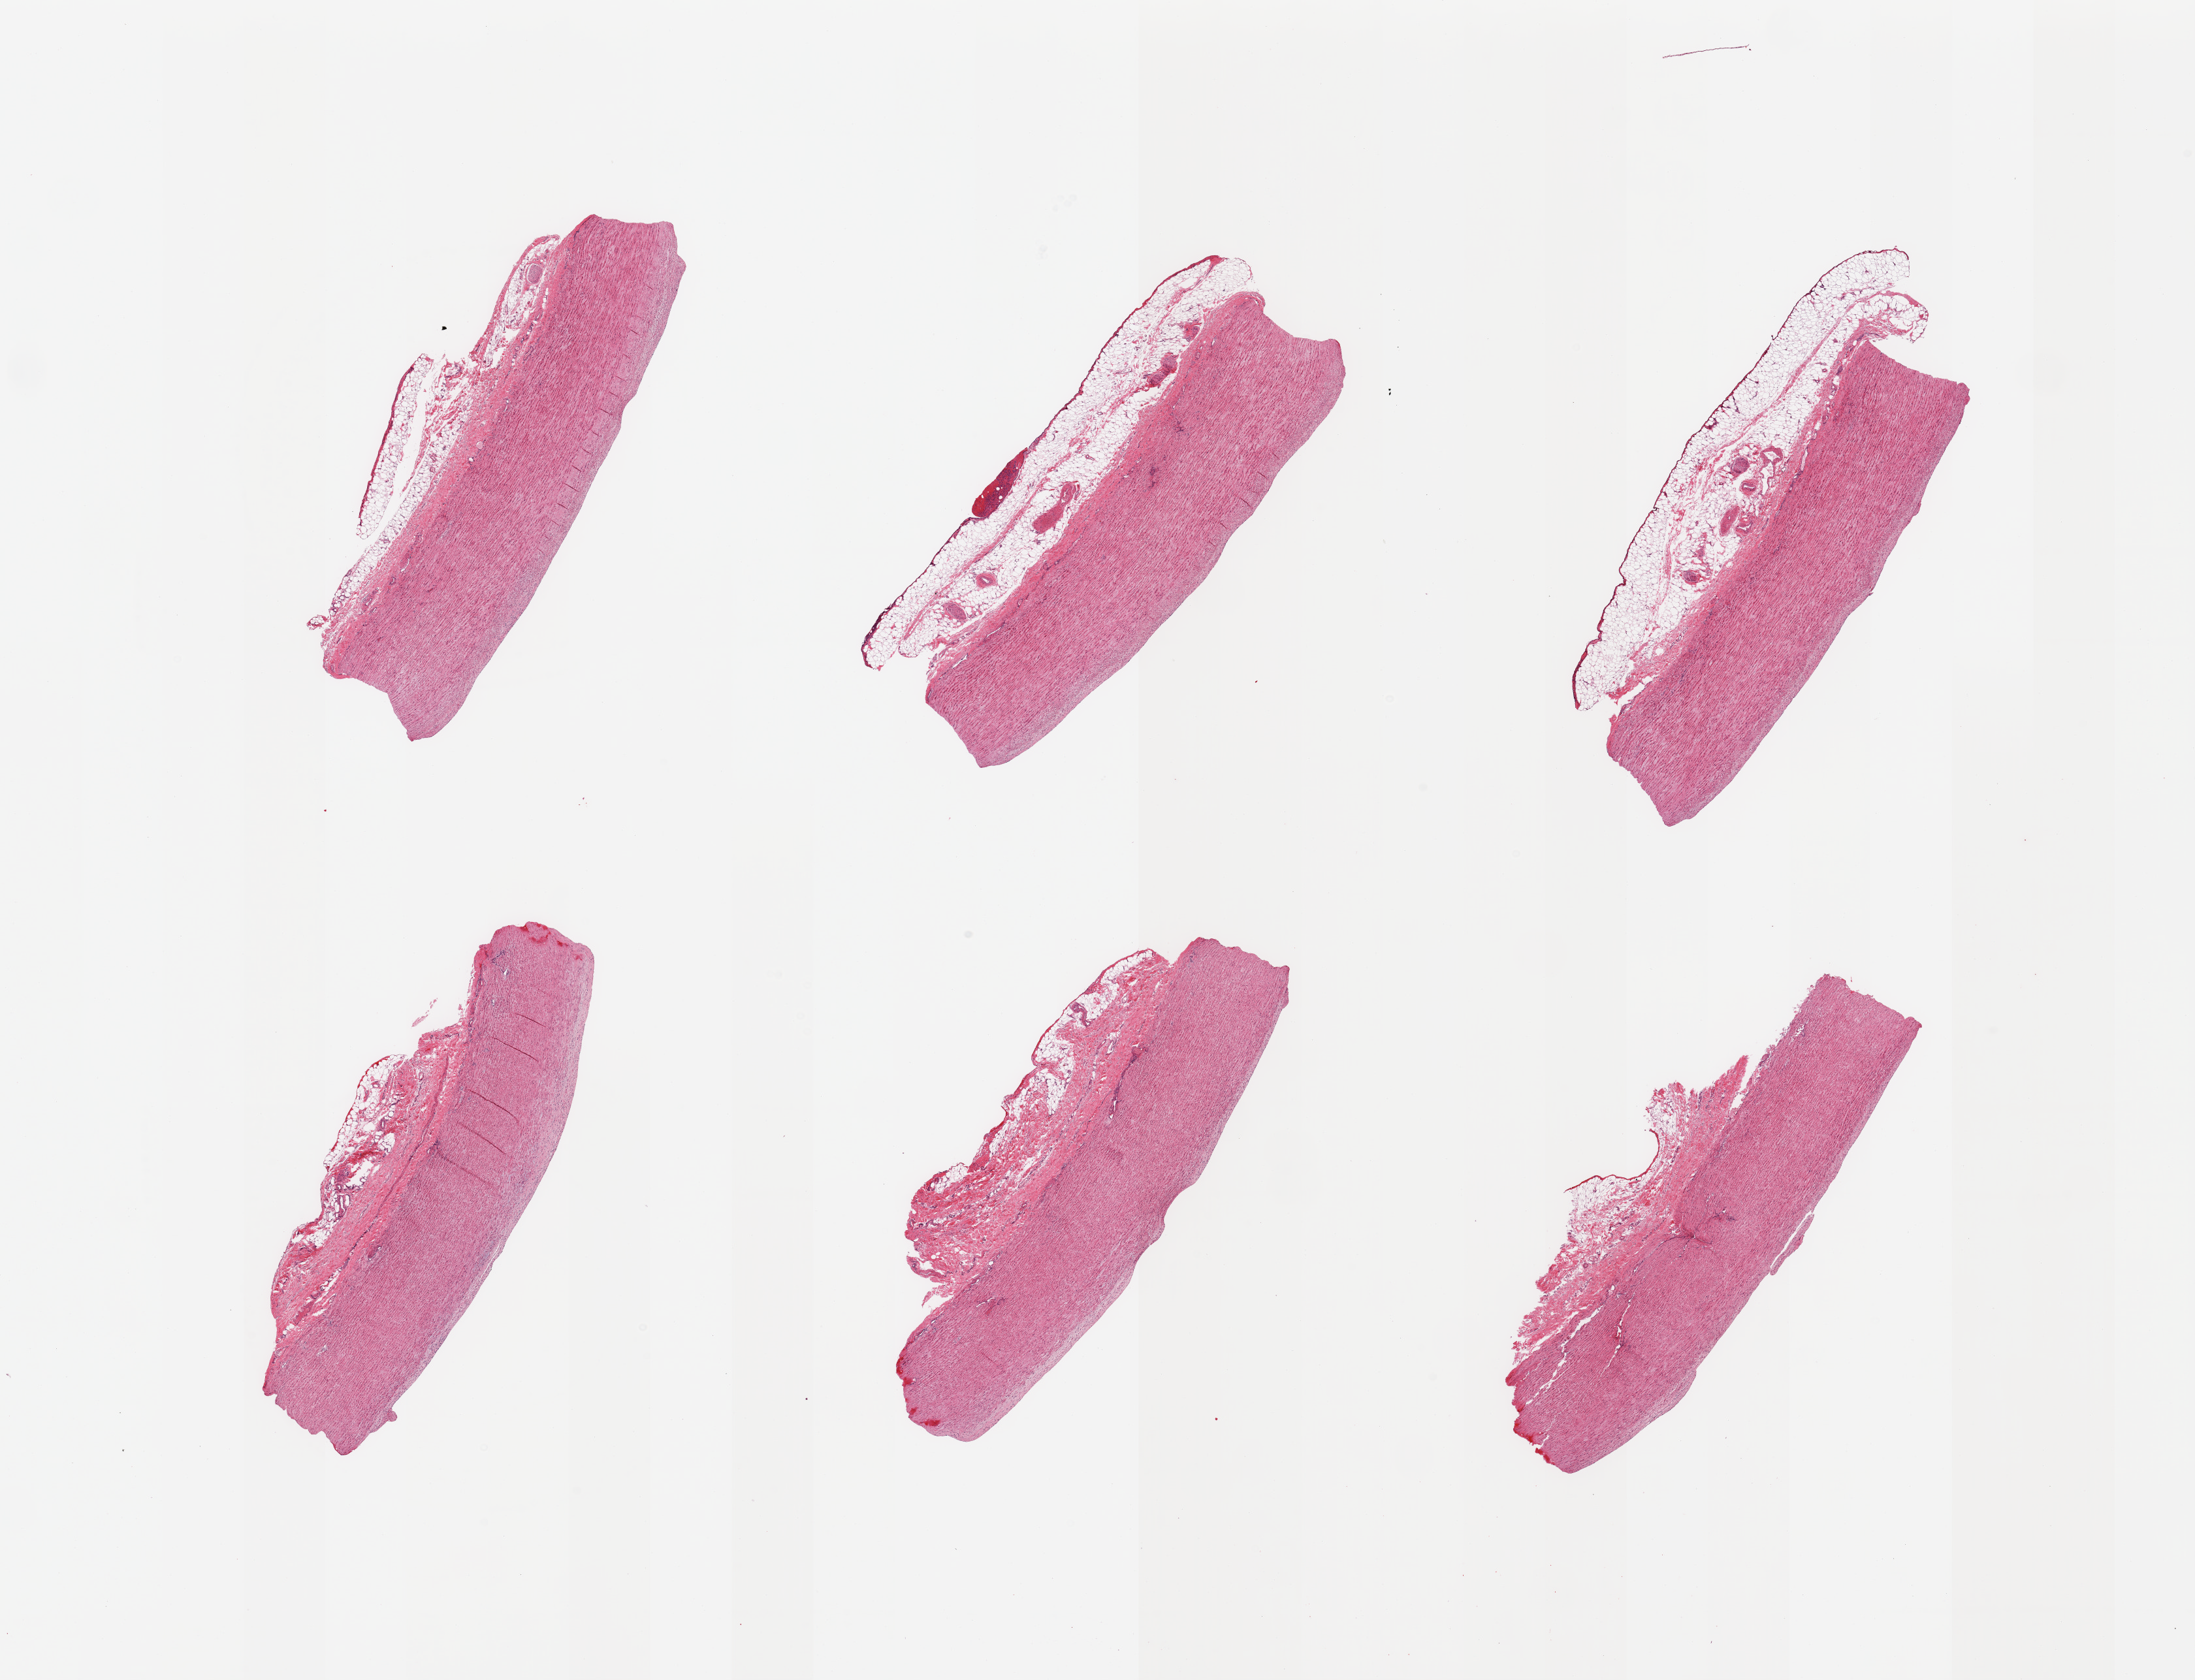
Haematoxylin and eosin whole-slide image, brightfield, whole scanned area (about 26.6 x 20.3 mm, acquisition: 20x scan) shown as a low-resolution overview. PAXgene-fixed, paraffin-embedded tissue. Sampled site (target tissue): aorta. Donor tissue sample. Donor sex: male.
• reviewer comment on this tissue sample: 6 pieces; minimal plaque; up to 1 mm fatty adventitia